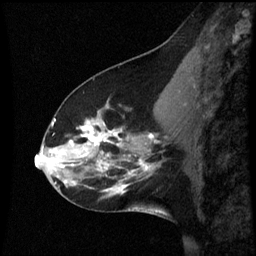
Breast MRI (dynamic contrast-enhanced), one sagittal slice; slice 24 of 60 in the series (ordered by position); dynamic contrast-enhanced series, image 2 of 3 at this slice position (ordered by acquisition); 1.5 T; TE 4.2 ms, TR 8.9 ms; 2 mm slice thickness; 256 × 256 image matrix. Female patient, age 45 years. Case-level facts recorded for this patient, not image findings: setting: breast cancer imaged before/during neoadjuvant chemotherapy; receptor status: HR-positive, HER2-negative.
Structures marked on this image (semi-automatically segmented with operator editing):
- analysis volume of interest (the breast-tissue region the enhancement analysis was run in; not a lesion): bounding box [x1, y1, x2, y2] px = [46, 94, 171, 205]
- tumour enhancement mask (voxels above the 70 % enhancement threshold inside the analysis volume of interest): [46, 120, 157, 183]